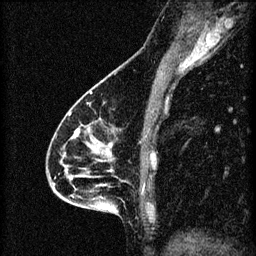
Breast MRI (dynamic contrast-enhanced), one sagittal slice. Slice 31 of 60 in the series (ordered by position). 3 images stored at this slice position (order not interpretable as contrast timing). 1.5 T. TE 4.2 ms, TR 8.2 ms. 256 × 256 image matrix, field of view 180 × 180 mm. Female patient, age 46 years.
Structures marked on this image (semi-automatically segmented with operator editing):
- analysis volume of interest (the breast-tissue region the enhancement analysis was run in; not a lesion): bounding box [x1, y1, x2, y2] px = [55, 114, 148, 209]
- tumour enhancement mask (voxels above the 70 % enhancement threshold inside the analysis volume of interest): [69, 114, 110, 171]